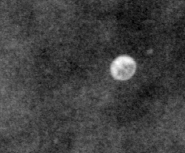
Crop from a digitized film mammogram around one marked abnormality, right breast, MLO view.
Calcifications, morphology round and regular / lucent center / punctate, distribution diffusely scattered; BI-RADS assessment category 2; subtlety rating 5 on a 1 (subtle) to 5 (obvious) scale; benign; no additional work-up was recommended (benign without callback).